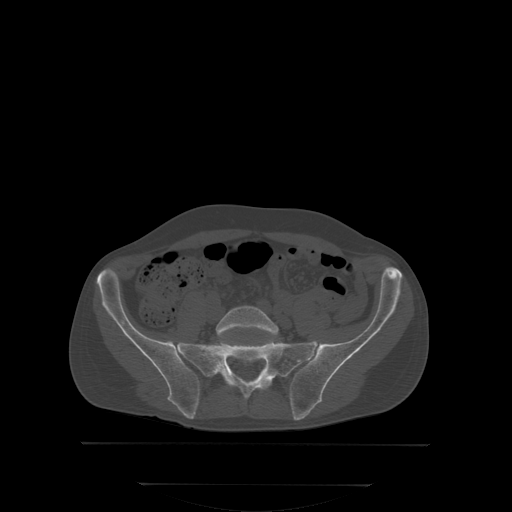
CT including the spine, one axial slice; position 87 of 350 along the scan axis; bone window (W 1800 / L 400 HU); 2.5 mm slice thickness; 512 × 512 image matrix, field of view 500 × 500 mm. Male patient, age 58 years. From the clinical record (not read from this slice): primary cancer: prostate; vertebrae with lytic lesions (as recorded): L1.
Outlined on this slice (semi-automatic segmentation, software-assisted and operator-edited):
- L5 vertebra: bounding box <216,305,278,345> (left, top, right, bottom; pixels)